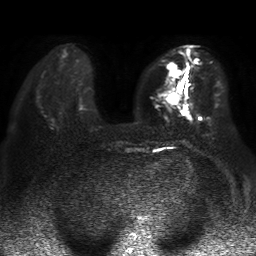
Breast MRI, one axial slice; slice 15 of 50 in the series (ordered by position); diffusion-weighted series; image 2 of 4 stored at this slice position (different b-values; order by instance number); 1.5 T; 4 mm slice thickness; 256 × 256 image matrix, field of view 360 × 360 mm. Female patient.
Structures marked on this image (expert manual segmentation):
- tumour on diffusion-weighted imaging: box from (x=167, y=63) to (x=180, y=103) px